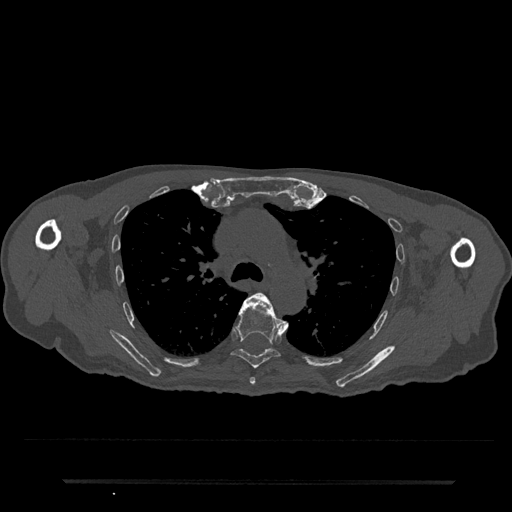
CT including the spine, one axial slice. Position 537 of 797 along the scan axis. 120 kVp. Bone window (W 1800 / L 400 HU). 0.5 mm slice thickness. 512 × 512 image matrix. Patient: male, 74 years. Case-level facts recorded for this patient, not image findings: primary cancer: prostate.
Annotated regions visible in this slice (semi-automatically segmented with operator editing):
- T5 vertebra: bounding box [x1, y1, x2, y2] px = [250, 293, 288, 385]
- T6 vertebra: [231, 293, 281, 369]